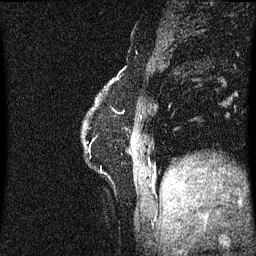
Breast MRI (dynamic contrast-enhanced), one sagittal slice; slice 11 of 60 in the series (ordered by position); dynamic contrast-enhanced series, image 2 of 3 at this slice position (ordered by acquisition); 1.5 T; TE 4.2 ms, TR 8.4 ms; 256 × 256 image matrix, field of view 200 × 200 mm. Patient: female, 60 years.
Structures marked on this image (semi-automatically segmented with operator editing):
- analysis volume of interest (the breast-tissue region the enhancement analysis was run in; not a lesion): bounding box <80,70,123,193> (left, top, right, bottom; pixels)
- tumour enhancement mask (voxels above the 70 % enhancement threshold inside the analysis volume of interest): <119,70,122,75>